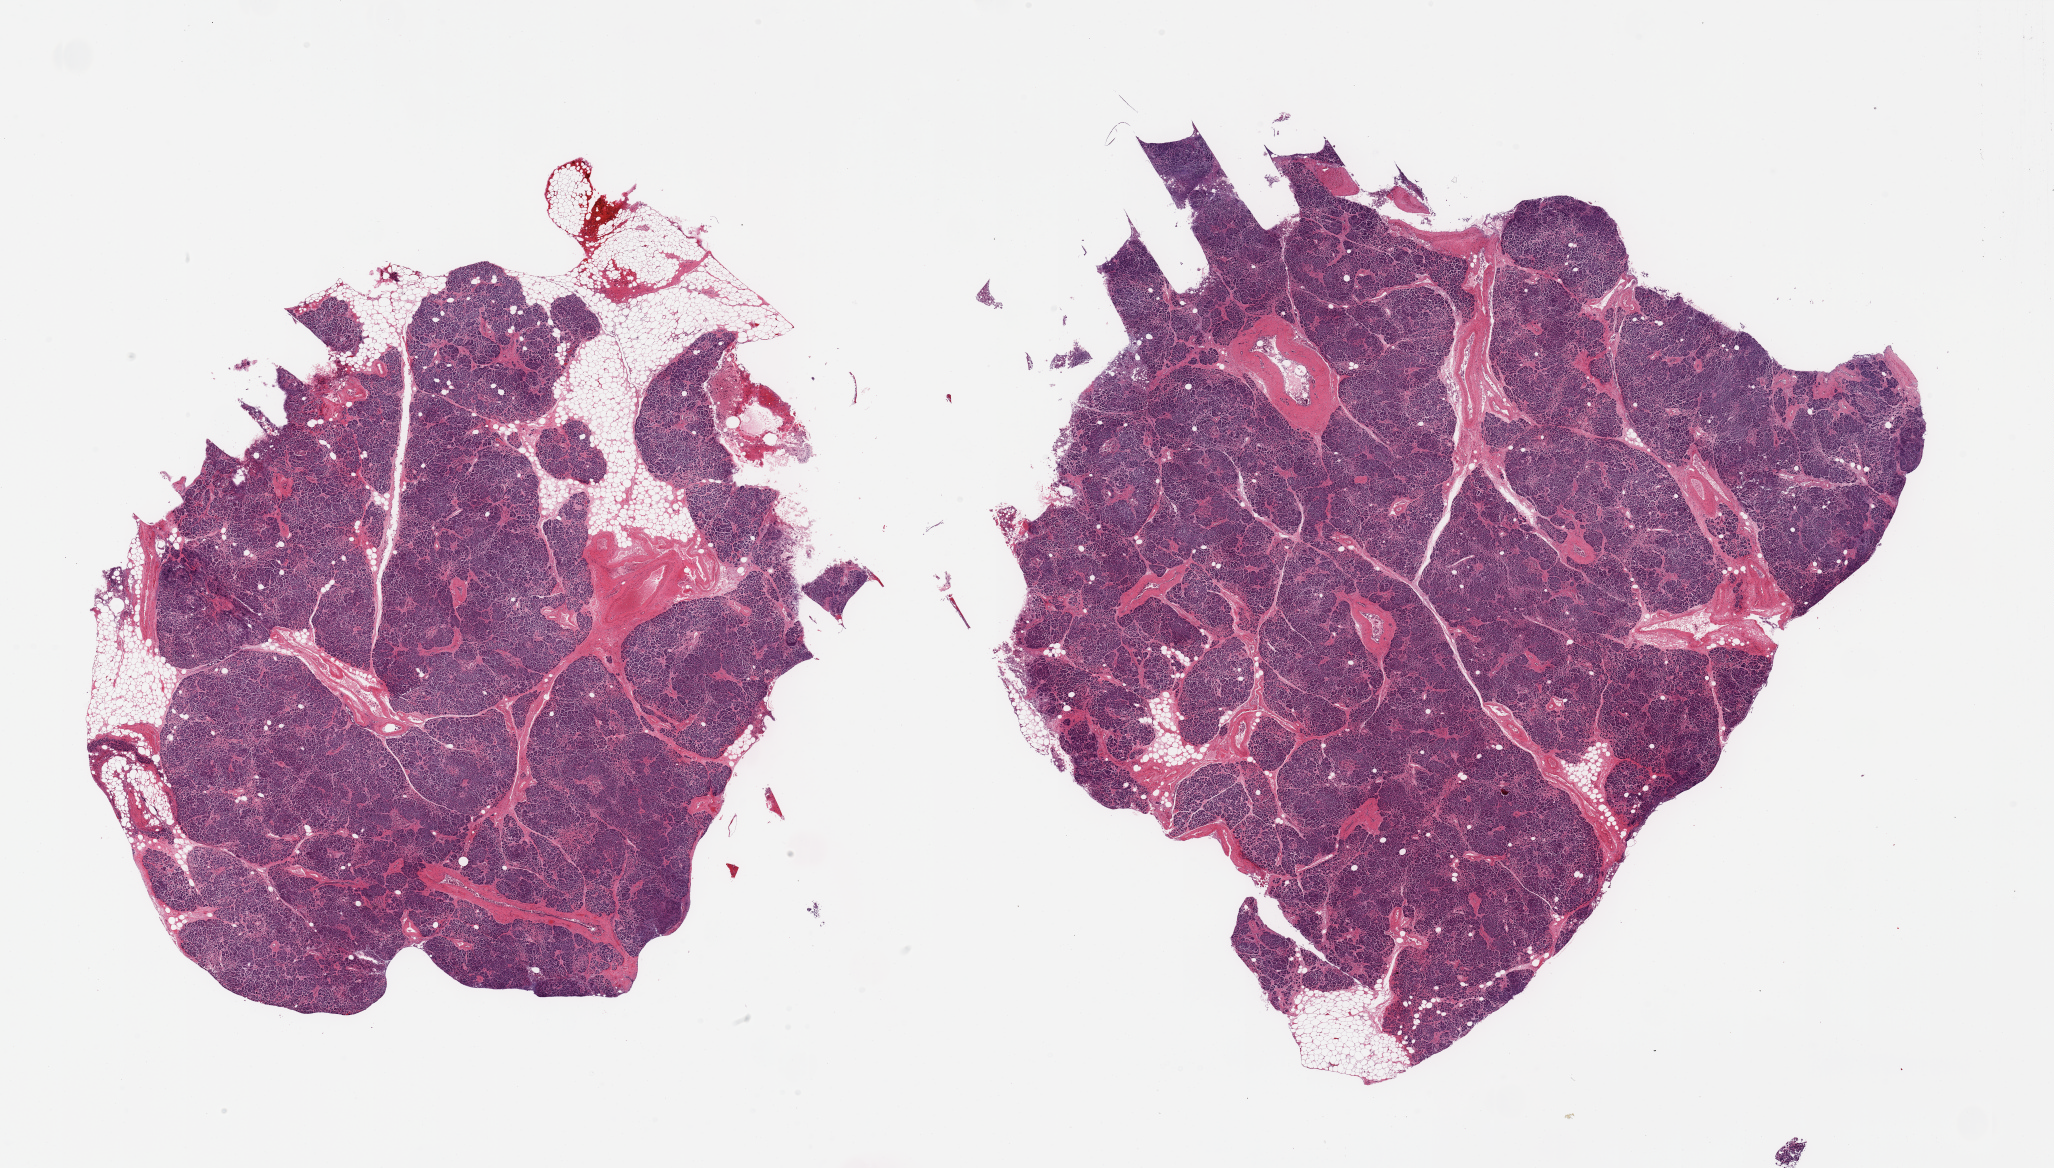
Whole-slide image, H&E stain — whole scanned area (about 32.5 x 18.5 mm) shown as a low-resolution overview; PAXgene-fixed, paraffin-embedded tissue; target tissue: pancreas; donor tissue sample. Male donor.
- review note (as recorded): 2 pieces, moderately advanced saponification. Islets still barely visible but degenerated